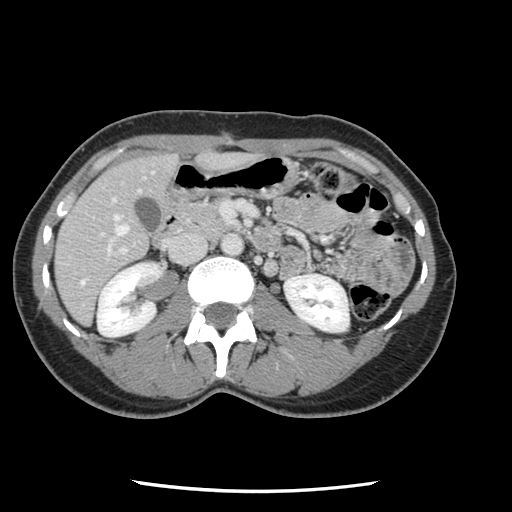
Contrast-enhanced abdominal CT, one axial slice. Position 44 of 134 along the scan axis. 120 kVp. Intravenous contrast given. Soft-tissue window (W 400 / L 40 HU). 512 × 512 image matrix. Female patient, age 43 years. From the clinical record (not read from this slice): diagnosis: colorectal cancer liver metastases, imaged before liver resection; multiple liver metastases: yes.
Annotated regions visible in this slice (manually delineated by an expert):
- hepatic veins: bounding box (x1, y1, x2, y2) in pixels: (81, 190, 140, 285)
- liver: (57, 155, 178, 323)
- planned liver remnant (the part of the liver to remain after resection): (56, 155, 177, 323)
- portal vein (with intrahepatic branches): (67, 201, 255, 306)